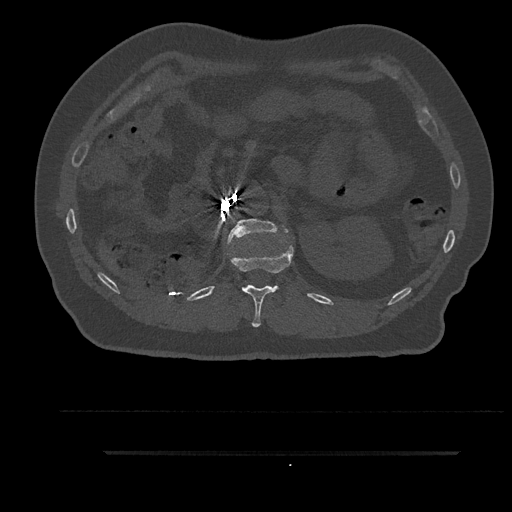
CT including the spine, one axial slice; bone window (W 1800 / L 400 HU); 0.5 mm slice thickness; 512 × 512 image matrix. Patient: male, 63 years. Case-level facts recorded for this patient, not image findings: primary cancer: renal.
Structures marked on this image (semi-automatically segmented with operator editing):
- L1 vertebra: bounding box [x1, y1, x2, y2] px = [227, 218, 288, 245]
- T12 vertebra: [228, 235, 294, 328]